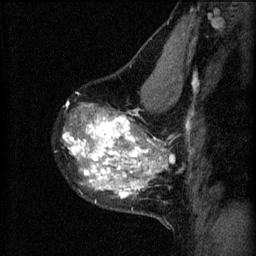
Breast MRI (dynamic contrast-enhanced), one sagittal slice. Slice 41 of 60 in the series (ordered by position). 3 images stored at this slice position (order not interpretable as contrast timing). 1.5 T. TE 4.2 ms, TR 8.2 ms. 256 × 256 image matrix, field of view 180 × 180 mm. Patient: female, 40 years.
Outlined on this slice (semi-automatic segmentation, software-assisted and operator-edited):
- analysis volume of interest (the breast-tissue region the enhancement analysis was run in; not a lesion): bounding box <62,76,179,219> (left, top, right, bottom; pixels)
- tumour enhancement mask (voxels above the 70 % enhancement threshold inside the analysis volume of interest): <62,106,165,199>